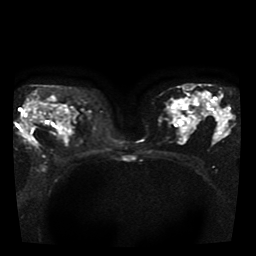
Breast MRI, one axial slice. Slice 24 of 41 in the series (ordered by position). Diffusion-weighted series; image 2 of 4 stored at this slice position (different b-values; order by instance number). 1.5 T. 256 × 256 image matrix, field of view 330 × 330 mm. Female patient.
Outlined on this slice (expert manual segmentation):
- tumour on diffusion-weighted imaging: bounding box [x1, y1, x2, y2] px = [23, 101, 38, 145]